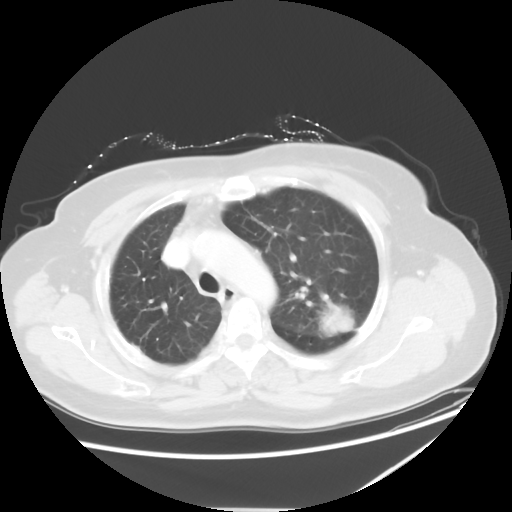
Chest CT, one axial slice; position 40 of 54 along the scan axis; reconstruction kernel STANDARD; 120 kVp; lung window (W 1500 / L -600 HU); 5 mm slice thickness; 512 × 512 image matrix, field of view 384 × 384 mm. Female patient, age 61 years. From the clinical record (not read from this slice): clinical TNM (as recorded): T1c N3 M1.
Annotated regions visible in this slice (rectangle marked by the reading radiologist):
- lung tumour (recorded histology: adenocarcinoma): box from (x=311, y=294) to (x=362, y=343) px